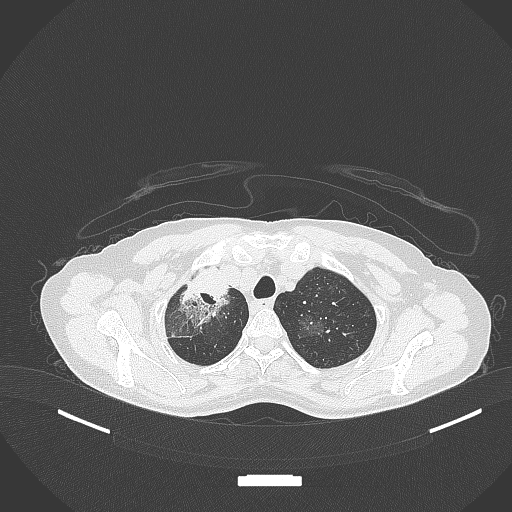
Chest CT, one axial slice. Position 277 of 284 along the scan axis. 120 kVp. Lung window (W 1500 / L -600 HU). 1 mm slice thickness. 512 × 512 image matrix, field of view 400 × 400 mm. Female patient, age 59 years. Case-level facts recorded for this patient, not image findings: clinical TNM (as recorded): T3 N0 M0.
Annotated regions visible in this slice (rectangle marked by the reading radiologist):
- lung tumour (recorded histology: adenocarcinoma): bounding box [x1, y1, x2, y2] px = [174, 265, 232, 327]